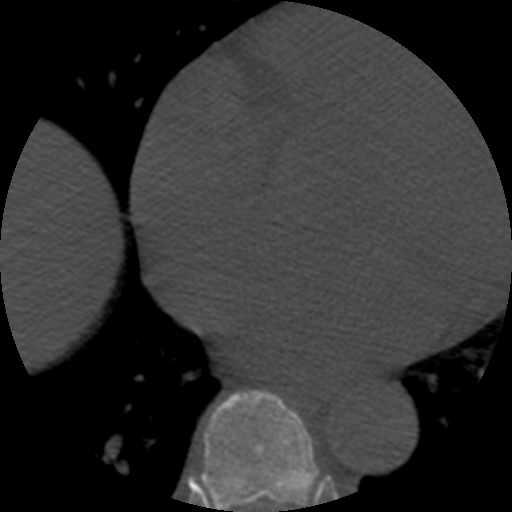
CT including the spine, one axial slice; position 324 of 508 along the scan axis; 120 kVp; bone window (W 1800 / L 400 HU); 1.25 mm slice thickness; 512 × 512 image matrix, field of view 160 × 160 mm. Patient age 57 years. Case-level facts recorded for this patient, not image findings: primary cancer: prostate.
Structures marked on this image (semi-automatic segmentation, software-assisted and operator-edited):
- T7 vertebra: bounding box <193,391,316,512> (left, top, right, bottom; pixels)